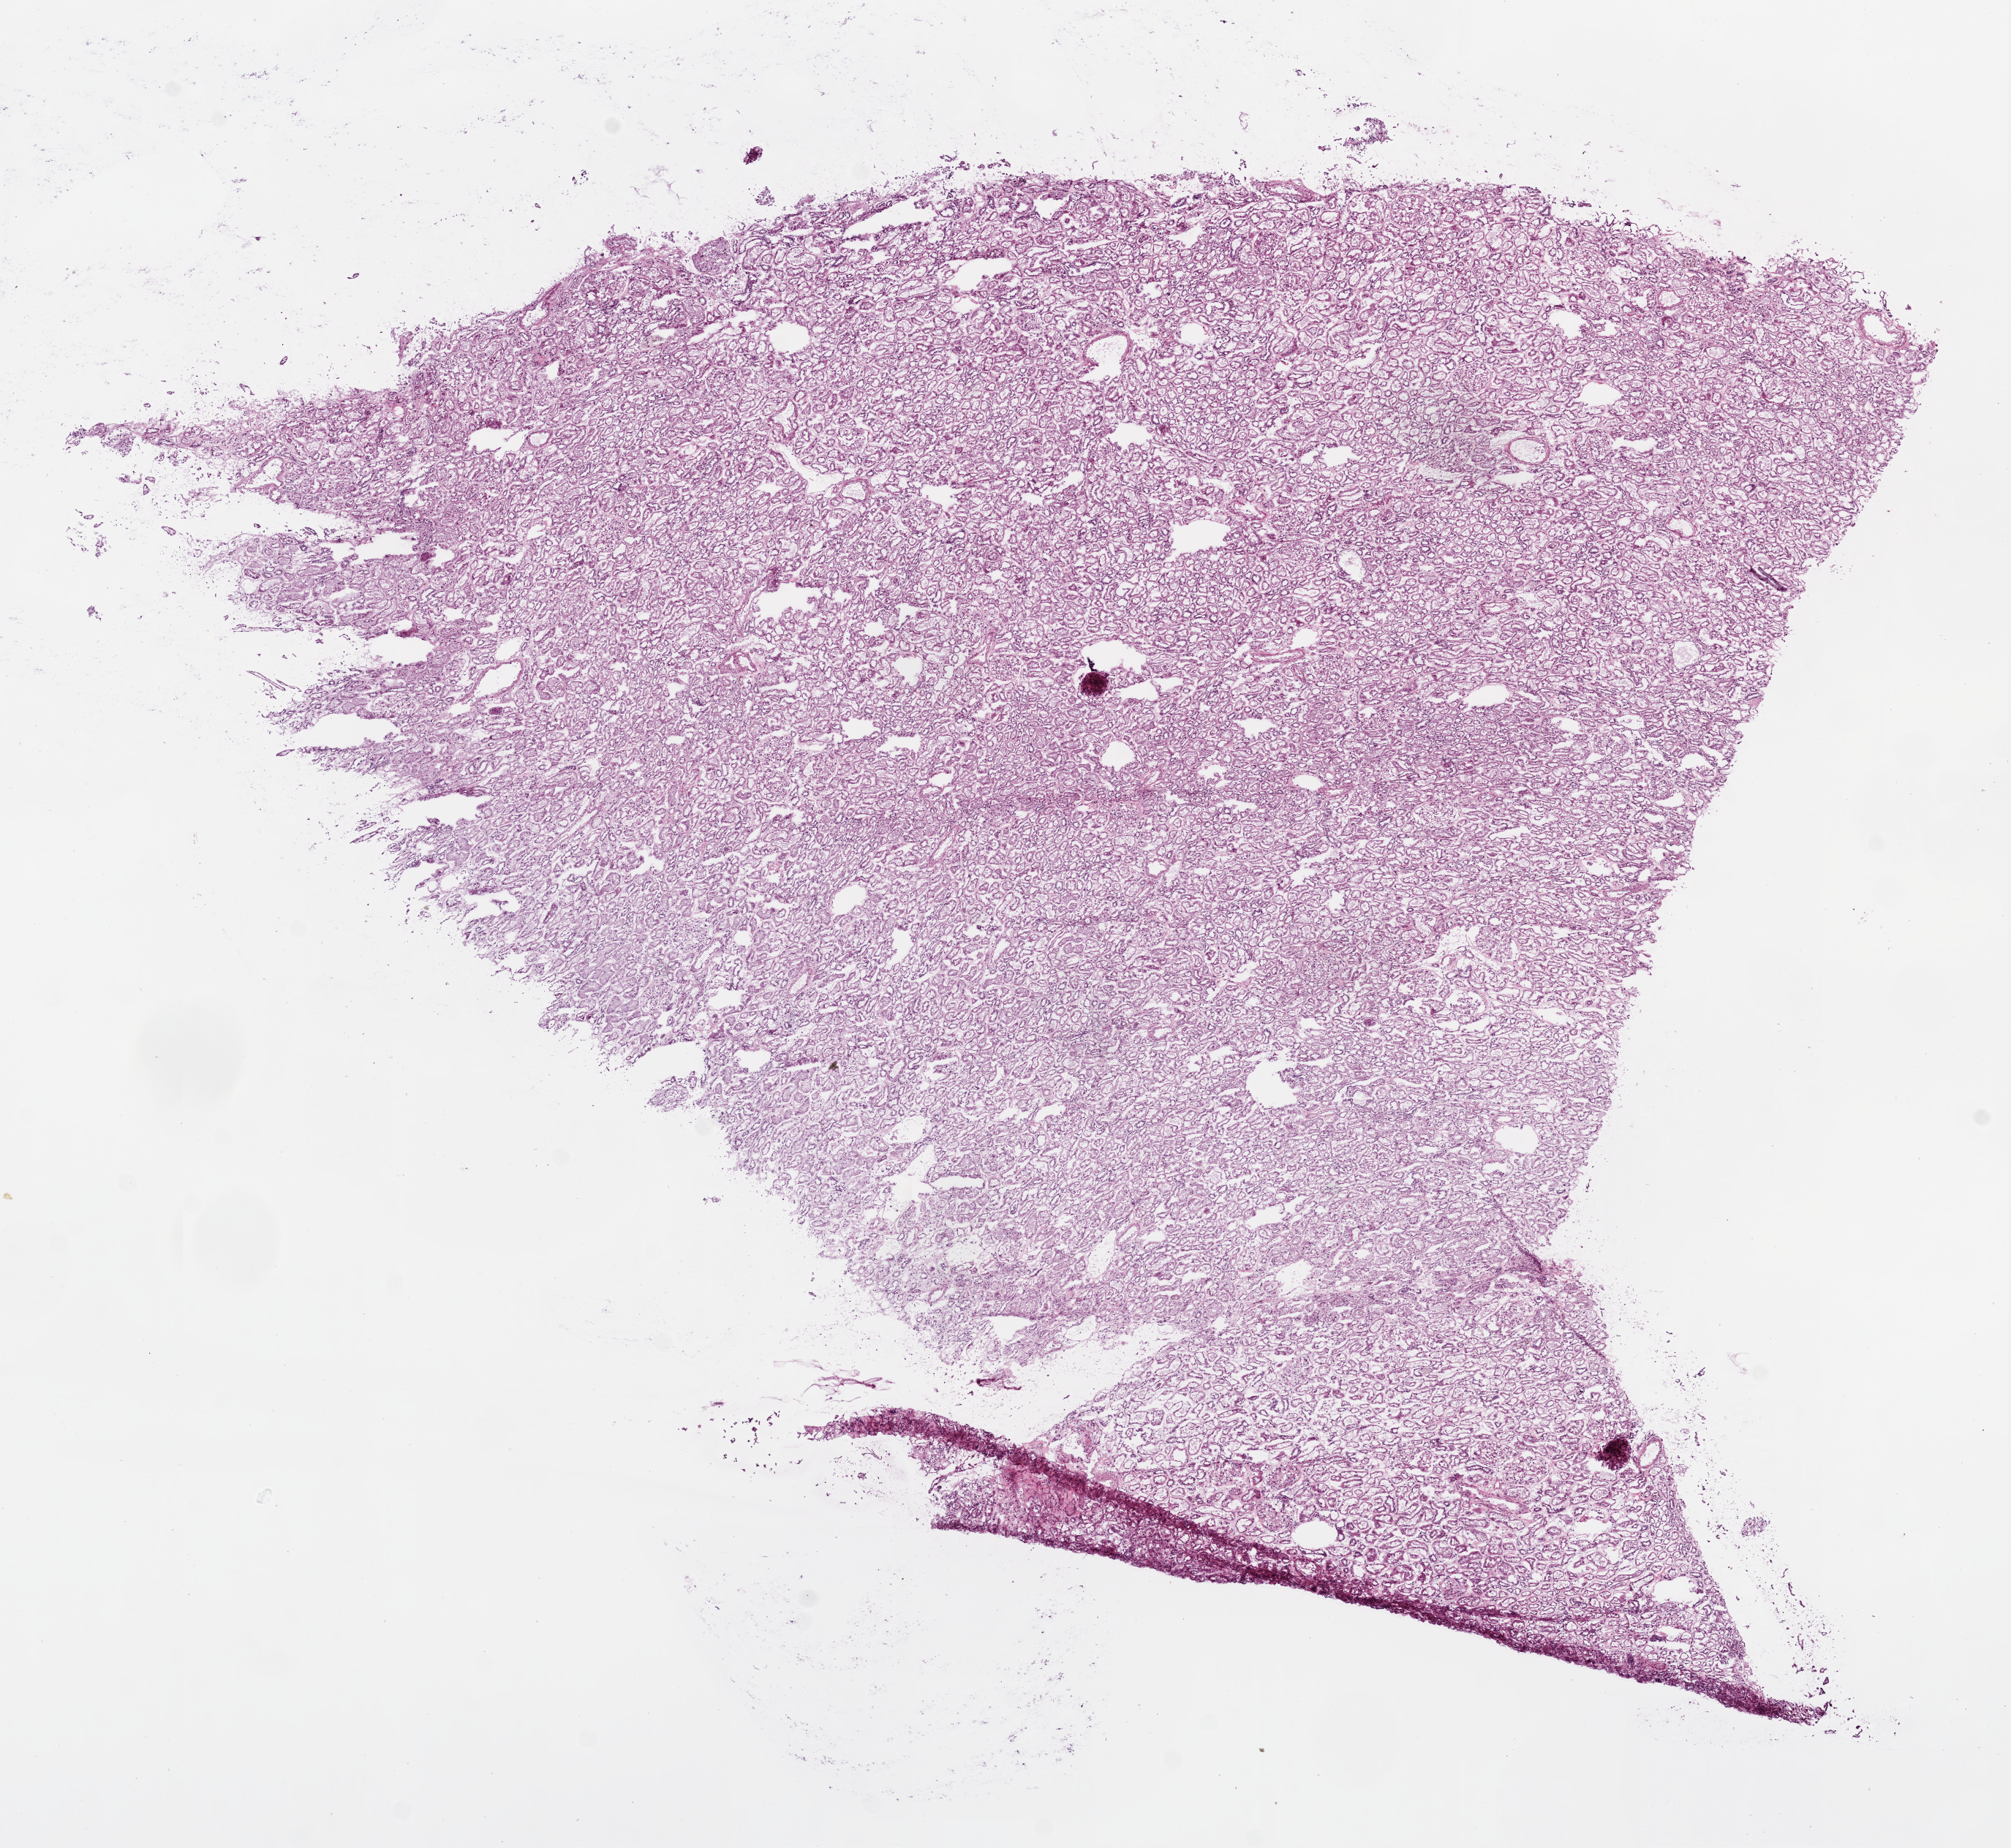
Hematoxylin and eosin (H&E) stained whole-slide image — a low-resolution overview of the entire scanned area, about 11.0 x 10.1 mm; frozen section from the bottom of the tissue portion; sample: solid tissue normal (non-tumour tissue), kidney. Male patient; age at initial diagnosis 51 years.
* this section: solid tissue normal sample (biorepository sample class)
* patient diagnosis: Clear cell adenocarcinoma, NOS